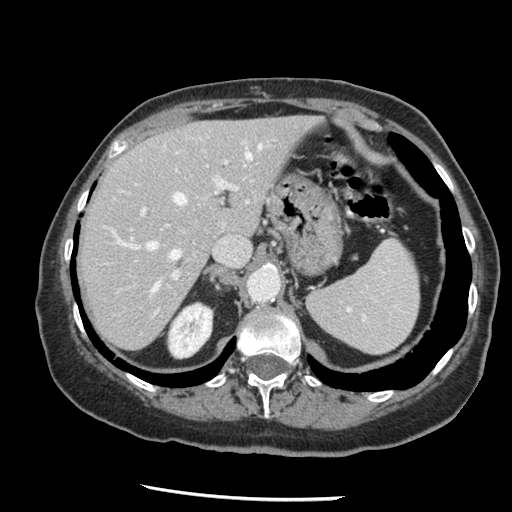
Contrast-enhanced abdominal CT, one axial slice. Position 96 of 148 along the scan axis. Reconstruction kernel STANDARD. 120 kVp. Soft-tissue window (W 400 / L 40 HU). 2.5 mm slice thickness. 512 × 512 image matrix, field of view 330 × 330 mm. Female patient, age 85 years. From the clinical record (not read from this slice): diagnosis: colorectal cancer liver metastases, imaged before liver resection.
Structures marked on this image (outlined manually by an expert reader):
- hepatic veins: bounding box [x1, y1, x2, y2] px = [118, 140, 269, 293]
- liver: [81, 117, 317, 349]
- planned liver remnant (the part of the liver to remain after resection): [81, 117, 317, 349]
- portal vein (with intrahepatic branches): [131, 159, 237, 280]